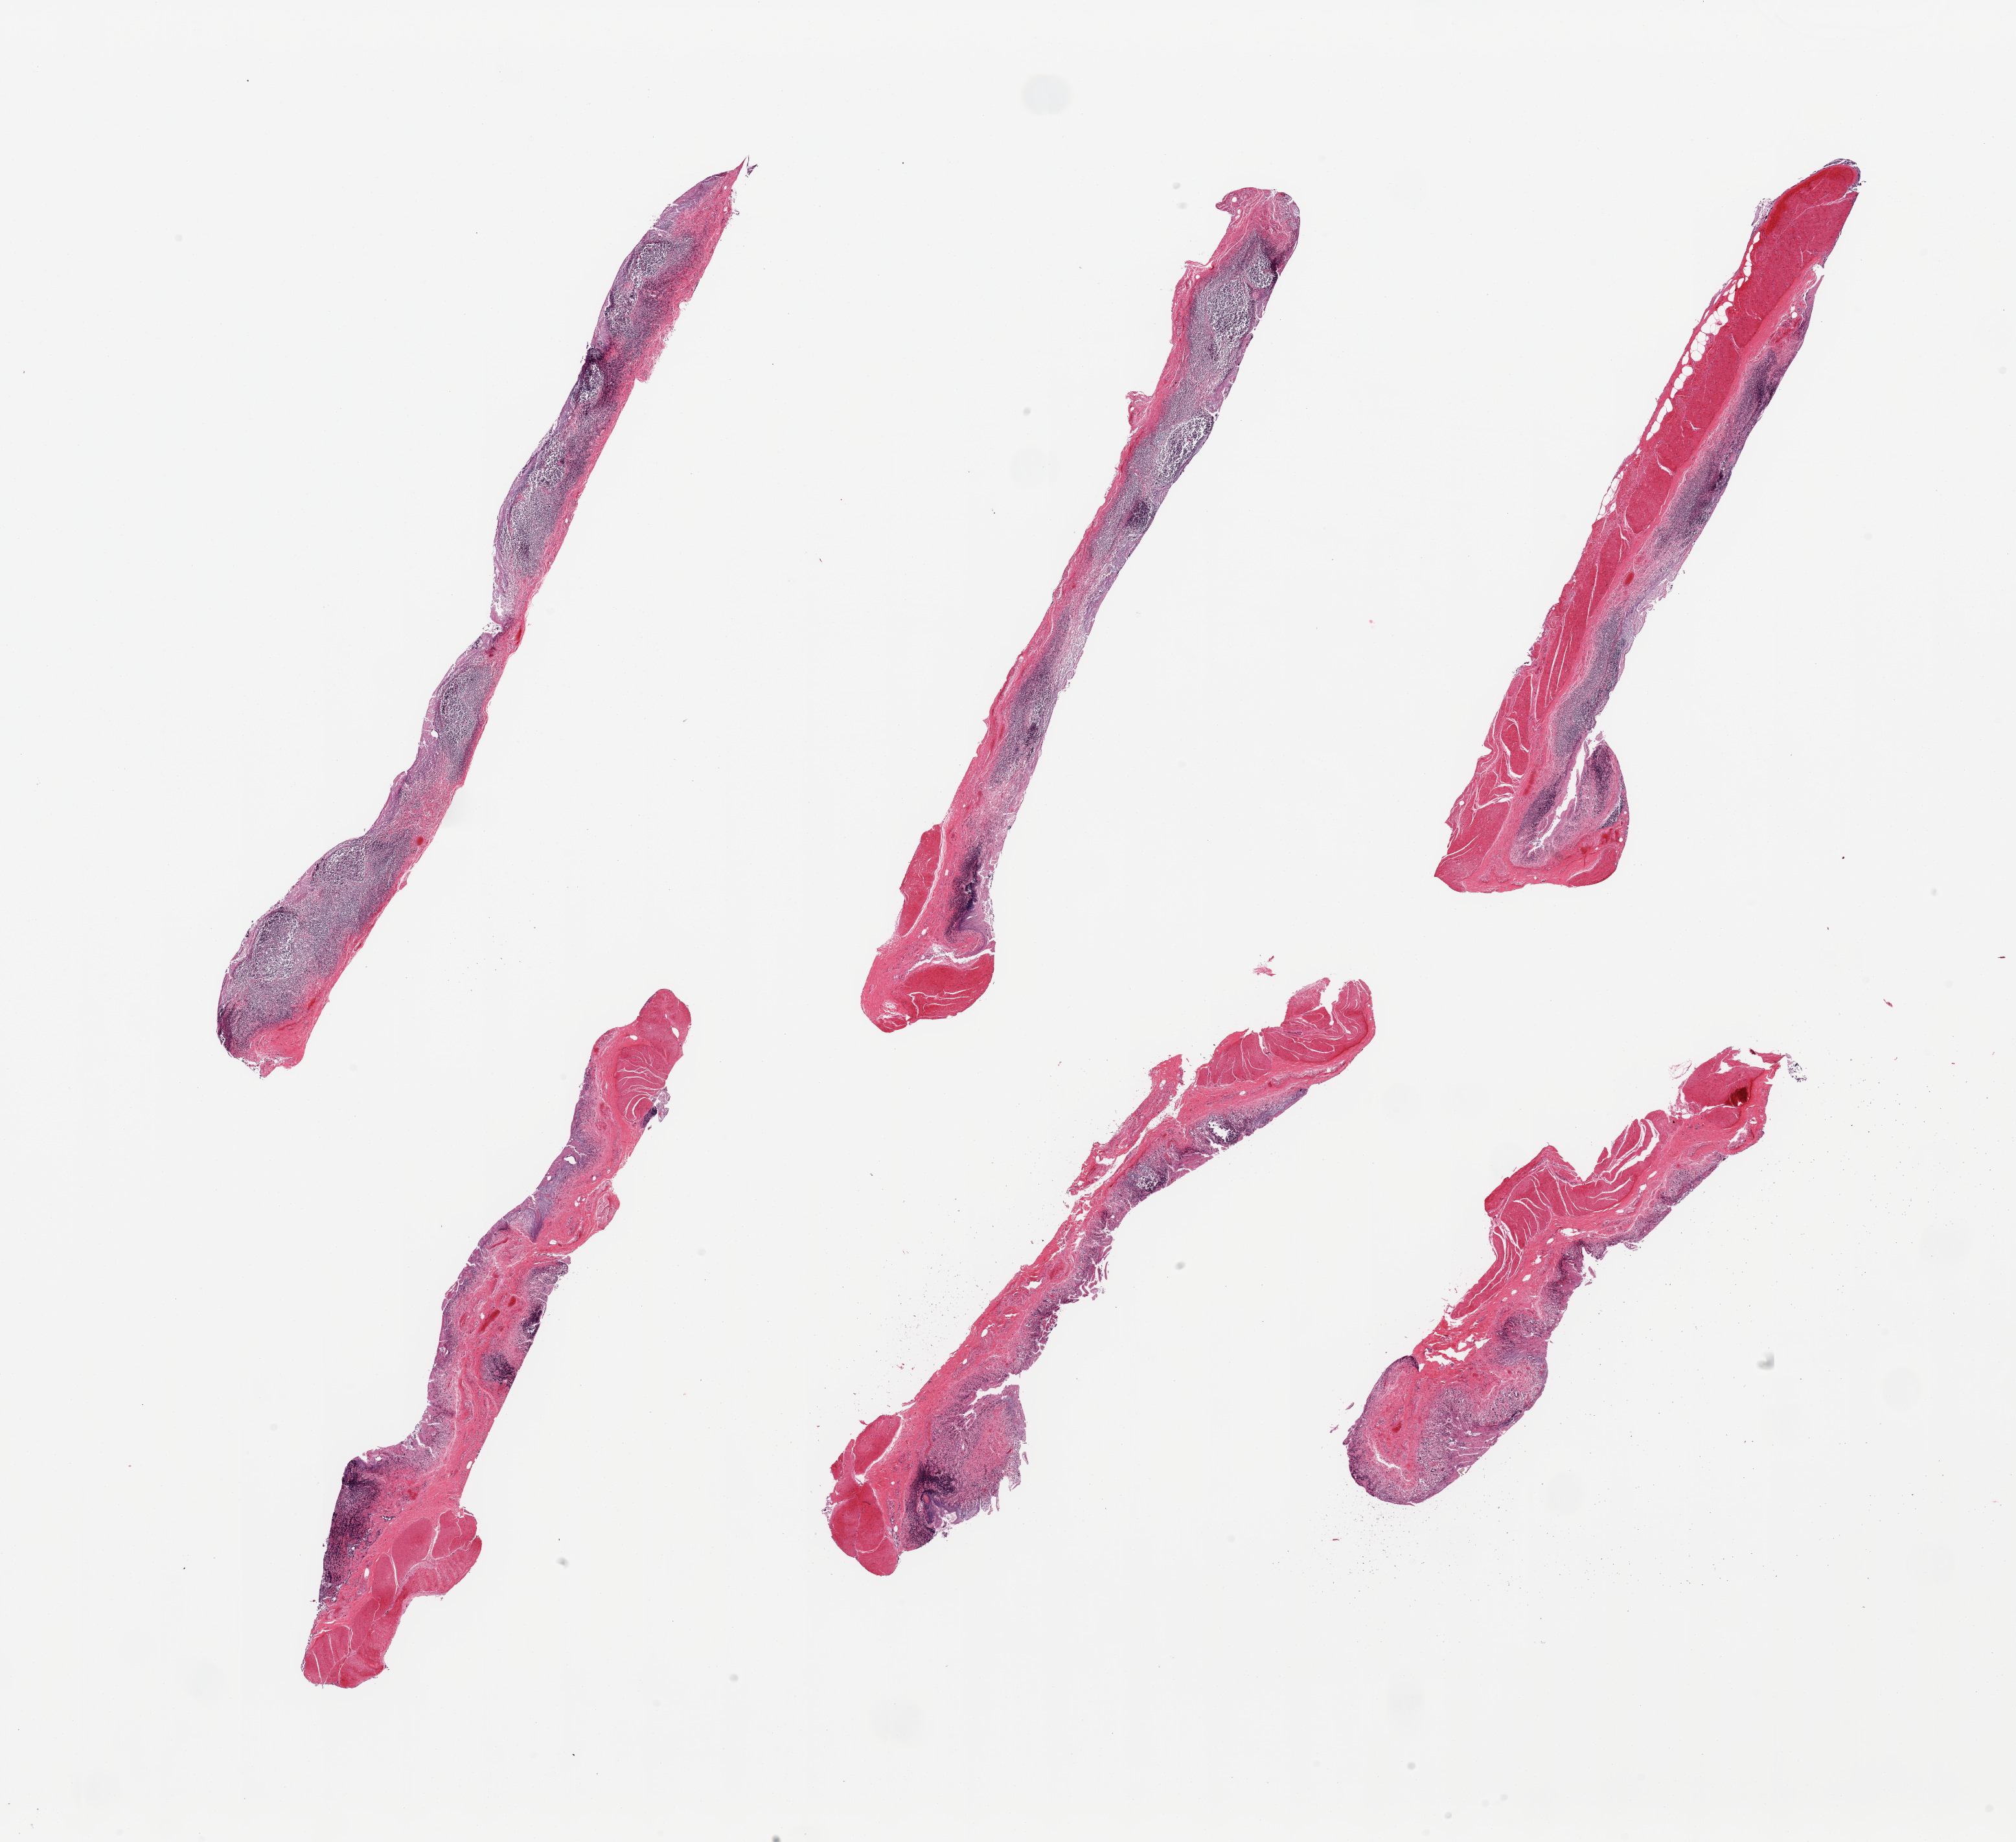
Whole-slide image, H&E stain, whole scanned area (about 24.6 x 22.5 mm, slide scanned at 20x) shown as a low-resolution overview. PAXgene-fixed, paraffin-embedded tissue. Section of ileum (target tissue). Donor tissue sample. Donor: male.
Reviewer comment on this tissue sample: 6 piece, glandular mucosa with advanced autolysis; residual target lymphoid aggregates are ~40% of tissue.s.